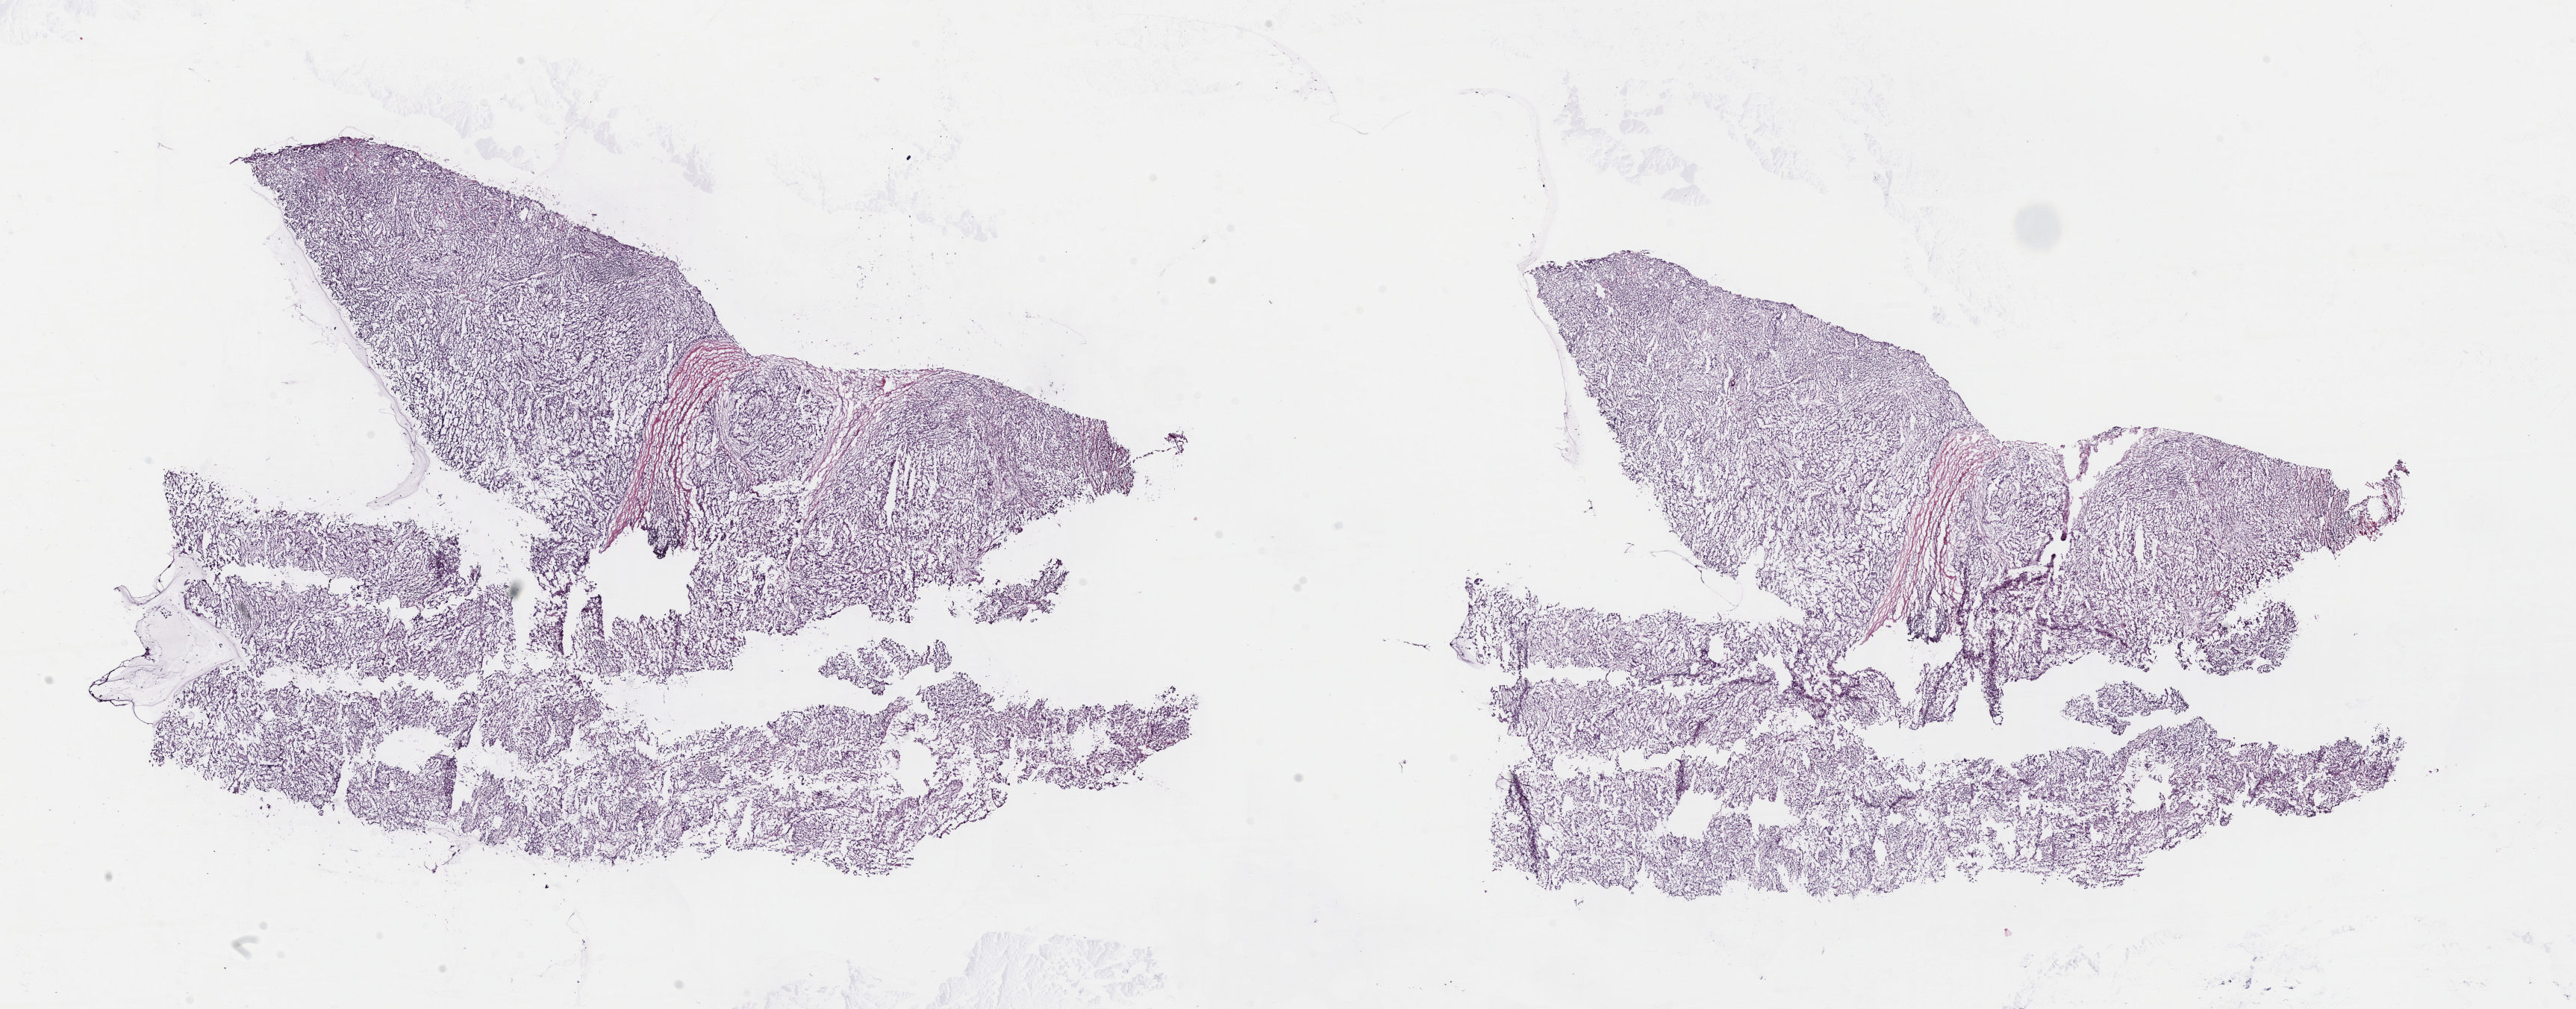
Hematoxylin and eosin (H&E) stained whole-slide image — whole scanned area (about 27.2 x 10.7 mm, from a 40x scan) shown as a low-resolution overview, frozen section from the top of the tissue portion, sample: primary tumour, kidney. Female patient; age at initial diagnosis 54 years. Pathologist review of this section (percent, as recorded): tumour cells 100%, tumour nuclei 80%, normal cells 0%, stromal cells 0%, necrosis 0%. Infiltration values recorded for this section: lymphocyte infiltration 1%, monocyte infiltration 0%, neutrophil infiltration 0%.
AJCC pathologic stage: III. Pathologic diagnosis: Papillary adenocarcinoma, NOS.